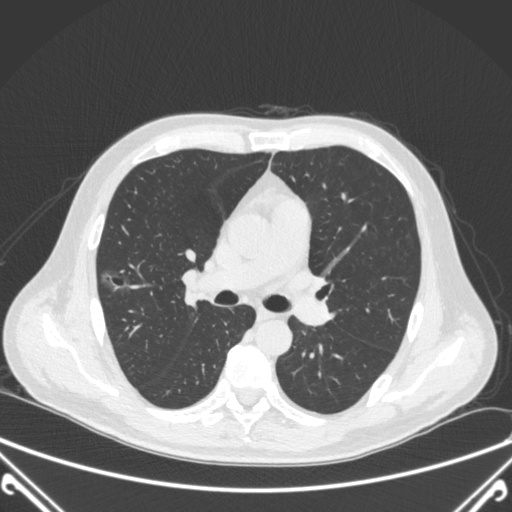
Chest CT, one axial slice; position 222 of 360 along the scan axis; 120 kVp; lung window (W 1500 / L -600 HU); 1 mm slice thickness; 512 × 512 image matrix, field of view 380 × 380 mm. Patient: male, 64 years. From the clinical record (not read from this slice): clinical TNM (as recorded): T1c N0 M0; histopathological grade: G2.
Outlined on this slice (bounding box drawn by a radiologist):
- lung tumour (recorded histology: adenocarcinoma): bounding box (x1, y1, x2, y2) in pixels: (98, 263, 133, 304)